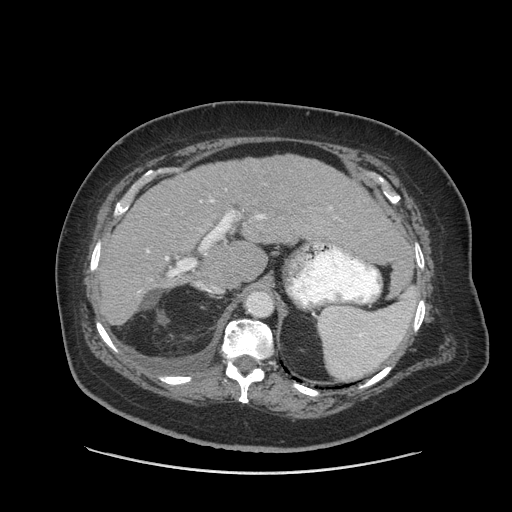
Contrast-enhanced abdominal CT (liver protocol), one axial slice; reconstruction kernel STANDARD; soft-tissue window (W 400 / L 40 HU); 2.5 mm slice thickness; 512 × 512 image matrix, field of view 420 × 420 mm. Case-level facts recorded for this patient, not image findings: diagnosis: hepatocellular carcinoma (patient treated with transarterial chemoembolisation; whether this scan precedes or follows treatment is not stated here); TNM stage (as recorded): Stage-I; Child-Pugh class: A.
Structures marked on this image (semi-automatic segmentation, software-assisted and operator-edited):
- liver parenchyma outside the tumour (the mass and vessels are separate outlines, so this box may not span the whole liver): box from (x=98, y=155) to (x=402, y=324) px
- liver vessels: (x=146, y=200)–(x=264, y=260)